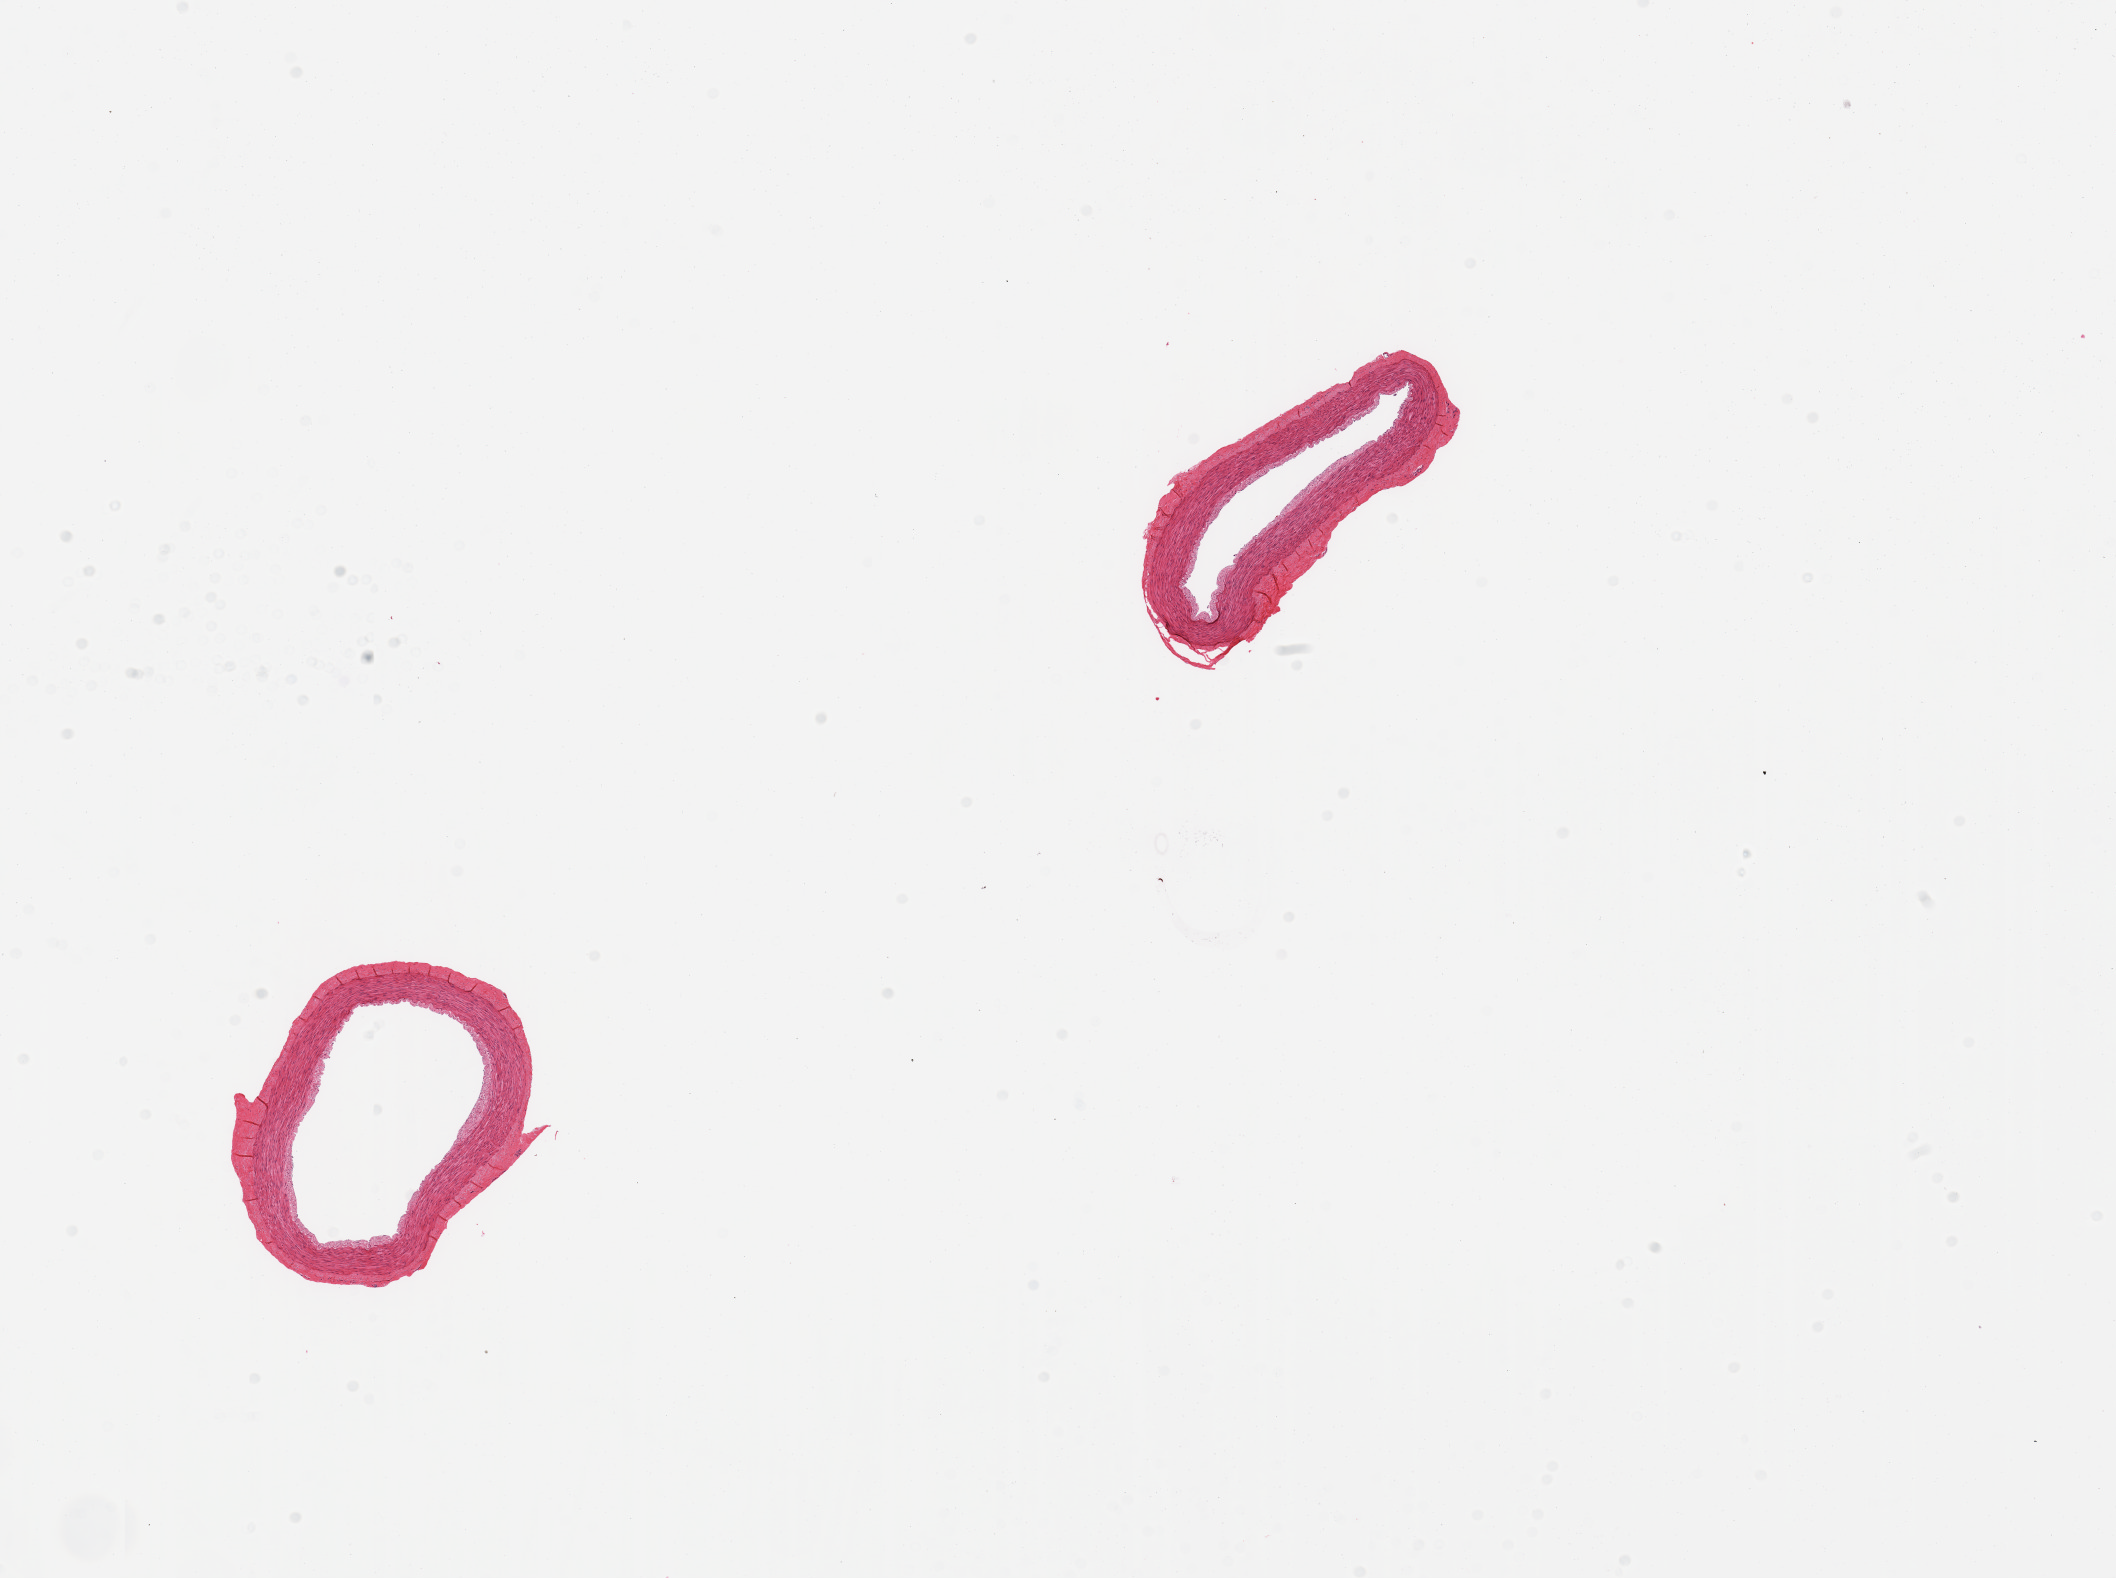
Whole-slide image, H&E stain, brightfield, whole scanned area (about 16.7 x 12.5 mm, acquisition: 20x scan) shown as a low-resolution overview; PAXgene-fixed, paraffin-embedded tissue; section of tibial artery (target tissue); donor tissue sample. Donor sex: male.
Reviewer comment on this tissue sample: 2 pieces, excellent specimens, no atherosis.